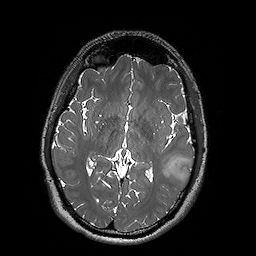
Brain MRI from a brain-tumour surgery series, one axial slice; position 91 of 192 along the scan axis; 1 mm slice thickness; 256 × 256 image matrix. From the clinical record (not read from this slice): histopathology: Oligodendroglioma; WHO grade: 2; IDH mutation: yes; tumour location: Left Posterior Temporal.
Structures marked on this image (manually delineated by an expert):
- tumour: bounding box [x1, y1, x2, y2] px = [159, 155, 193, 182]